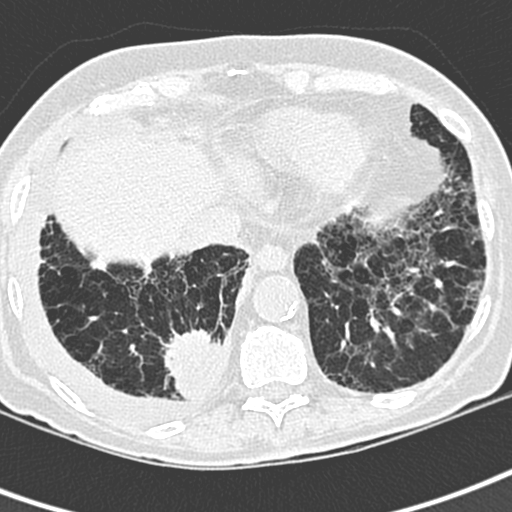
Low-dose screening chest CT, one axial slice; position 73 of 220 along the scan axis; lung window (W 1500 / L -600 HU); 1.3 mm slice thickness; 512 × 512 image matrix.
Annotated regions visible in this slice (outlined manually by an expert reader):
- lesion 1 (tumor, lower lobe of right lung): bounding box [x1, y1, x2, y2] px = [164, 329, 223, 400]